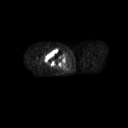
FDG PET of an extremity soft-tissue mass (from a PET/CT study), one axial slice. Slice 250 of 311 in the series (ordered by position). 3.27 mm slice thickness. 128 × 128 image matrix, field of view 700 × 700 mm. Patient: male, 50 years. Case-level facts recorded for this patient, not image findings: histological type: undifferentiated - pleiomorphic; grade: high; site of the primary tumour: right thigh.
Annotated regions visible in this slice (expert contour drawn on MRI and transferred to this co-registered scan by the dataset authors):
- gross tumour volume including surrounding oedema: bounding box [x1, y1, x2, y2] px = [42, 49, 64, 66]
- gross tumour volume (mass): [45, 49, 64, 66]